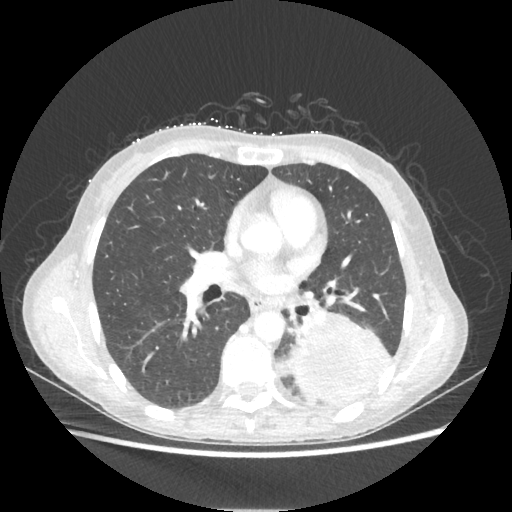
Chest CT, one axial slice. Slice 114 of 221 in the series (ordered by position). Lung window (W 1500 / L -600 HU). 1.25 mm slice thickness. 512 × 512 image matrix, field of view 360 × 360 mm. Patient: female, 53 years. From the clinical record (not read from this slice): clinical TNM (as recorded): T3 N0 M0.
Annotated regions visible in this slice (bounding box drawn by a radiologist):
- lung tumour (recorded histology: adenocarcinoma): bounding box <290,314,393,406> (left, top, right, bottom; pixels)